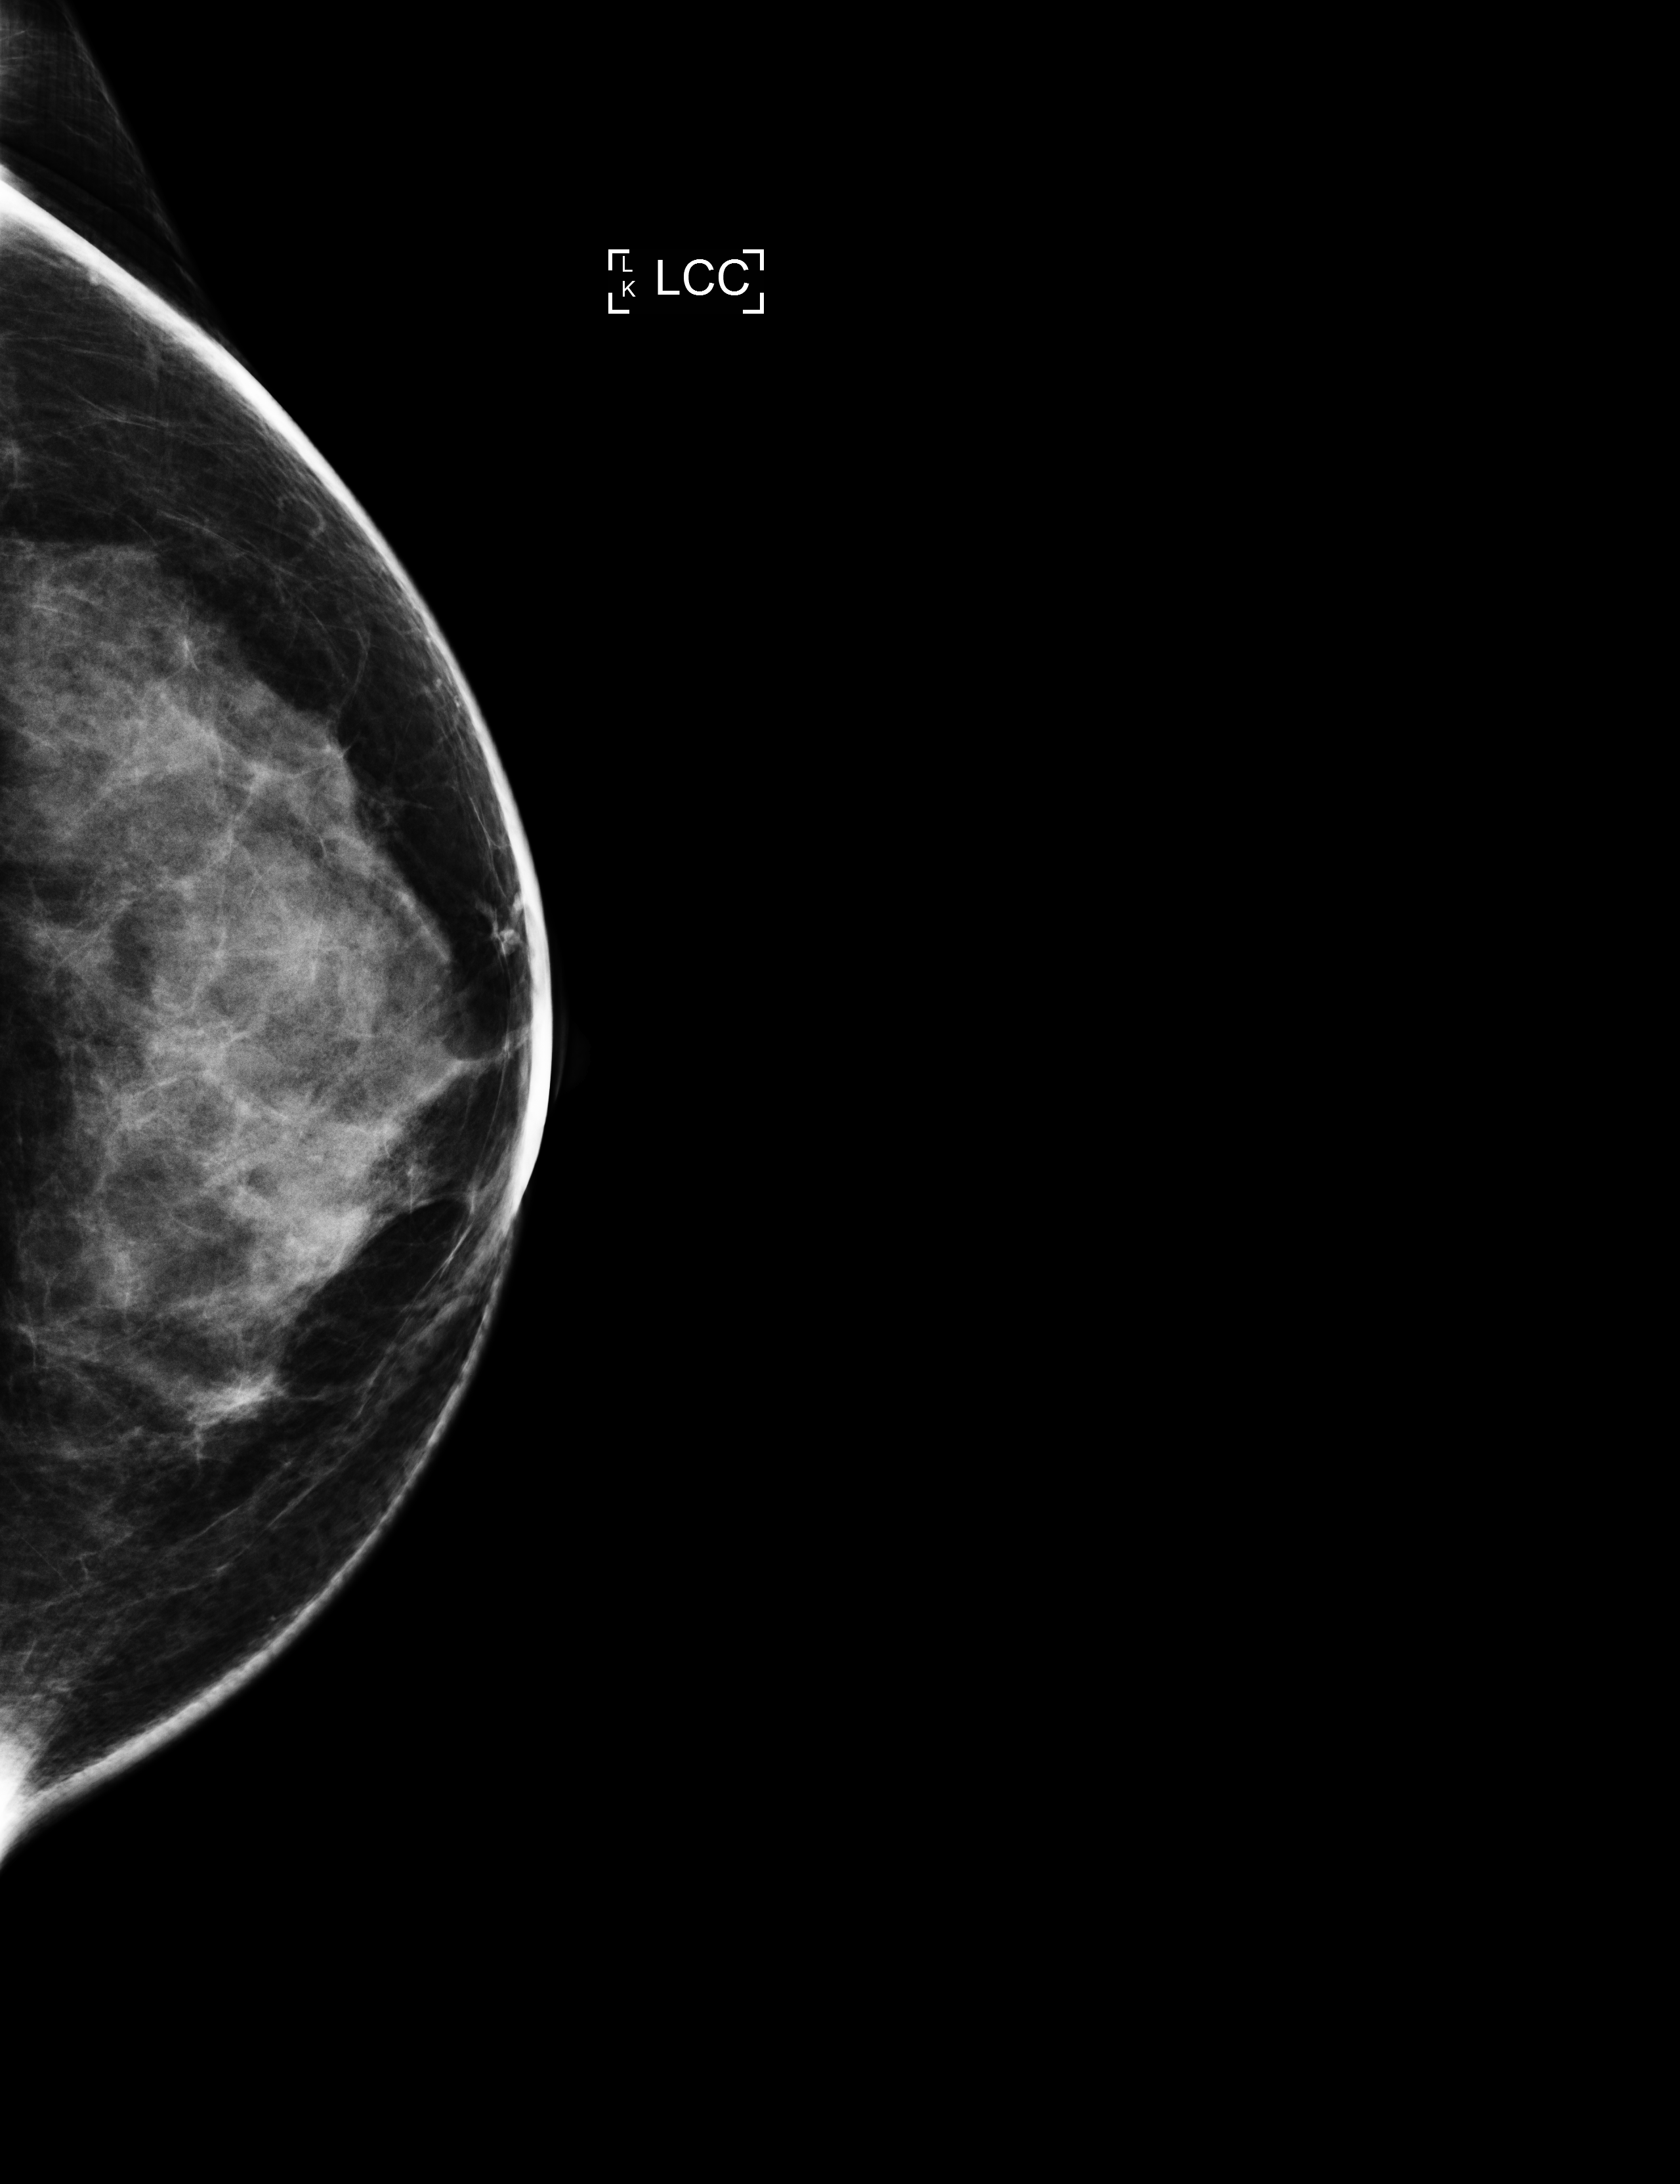
Annual screening mammography examination; system: Selenia Dimensions. Patient aged 44 years (female).
Image type: full-field digital mammogram. Breast: left. Projection: cranio-caudal projection.